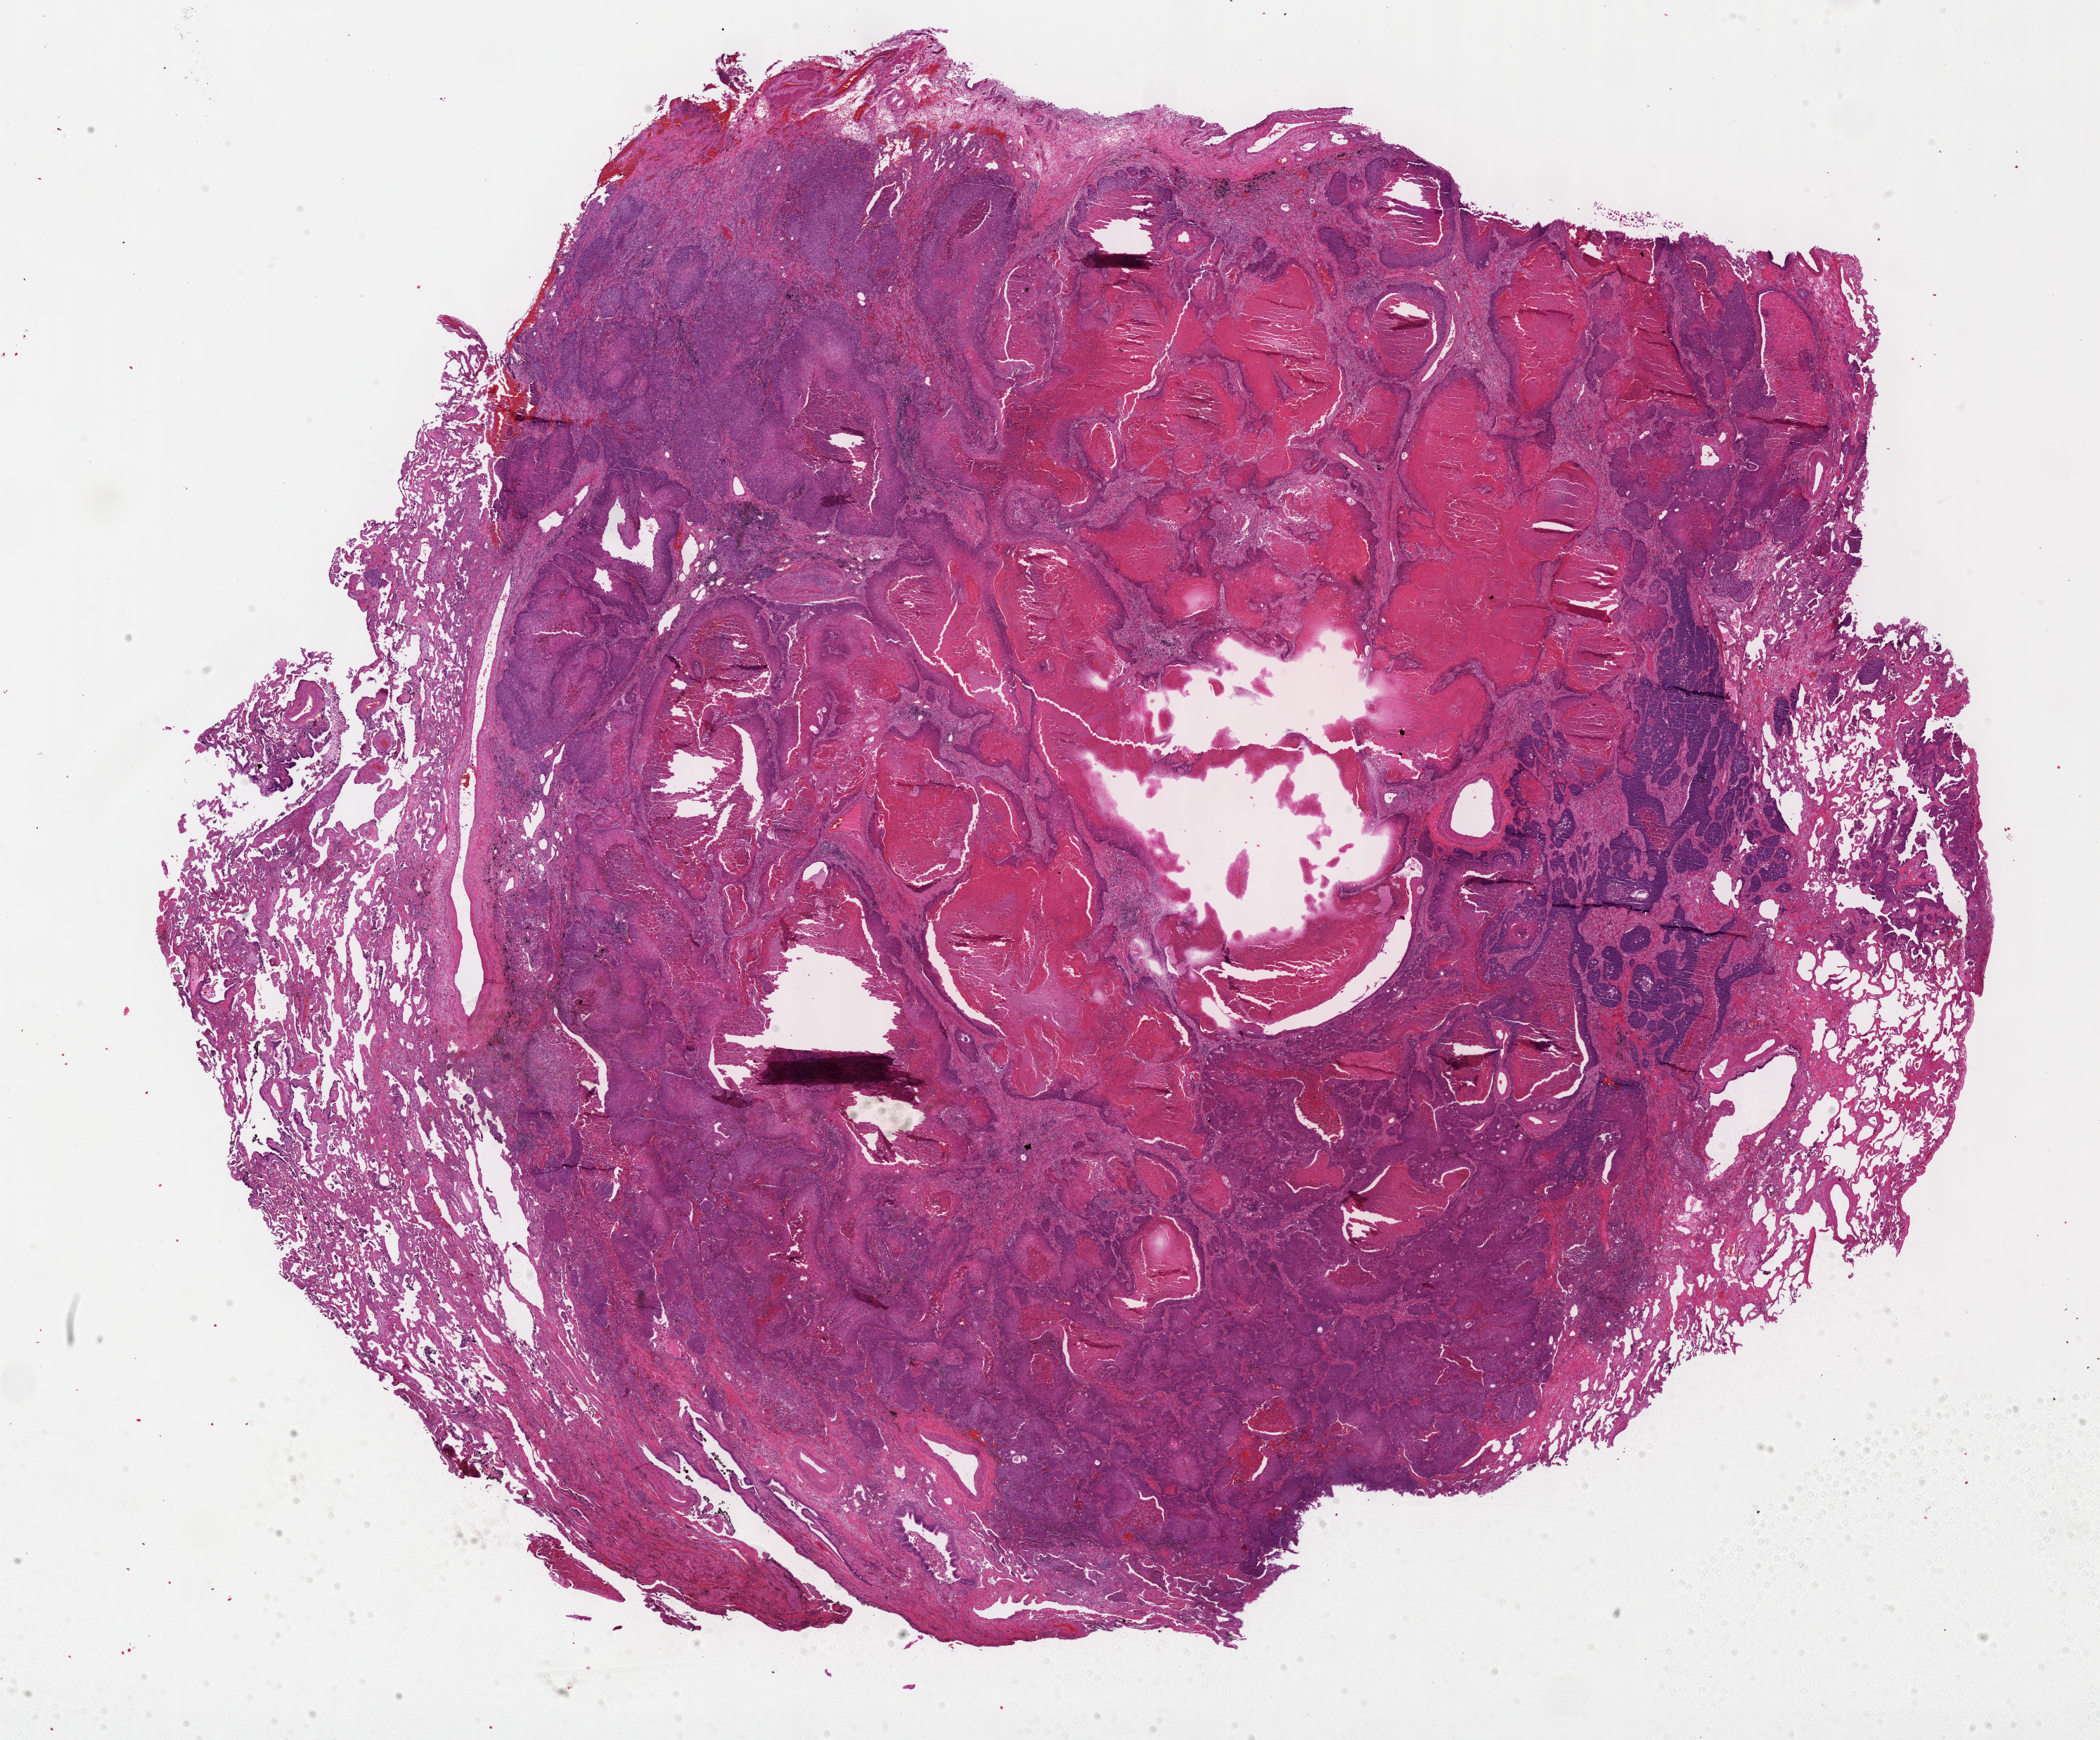
Whole-slide histology image, Hematoxylin and eosin (H&E) stained, whole scanned area (about 24.2 x 20.0 mm, slide scanned at 40x) shown as a low-resolution overview. FFPE section. Sample: primary tumour, lung. Male patient; age at initial diagnosis 67 years.
* histologic diagnosis: Squamous cell carcinoma, NOS (lower lobe, lung)
* TNM: T1a N1 MX
* AJCC pathologic stage: IIA (7th edition)
* laterality: right